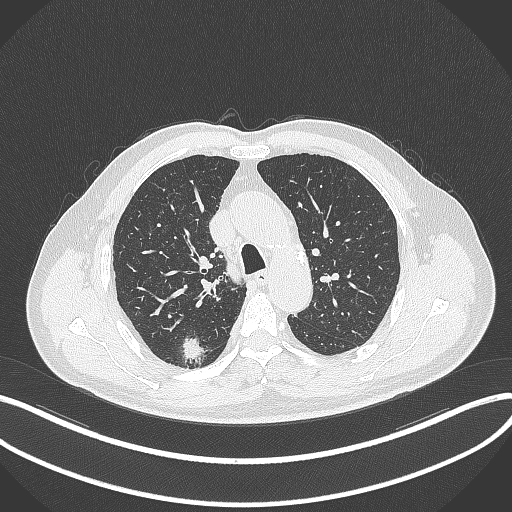
Chest CT, one axial slice; slice 265 of 359 in the series (ordered by position); reconstruction kernel B70f; 120 kVp; lung window (W 1500 / L -600 HU); 1 mm slice thickness; 512 × 512 image matrix. Patient: male, 69 years. From the clinical record (not read from this slice): clinical TNM (as recorded): T1b N0 M0; histopathological grade: G2-3.
Outlined on this slice (rectangle marked by the reading radiologist):
- lung tumour (recorded histology: adenocarcinoma): bounding box [x1, y1, x2, y2] px = [180, 335, 213, 363]